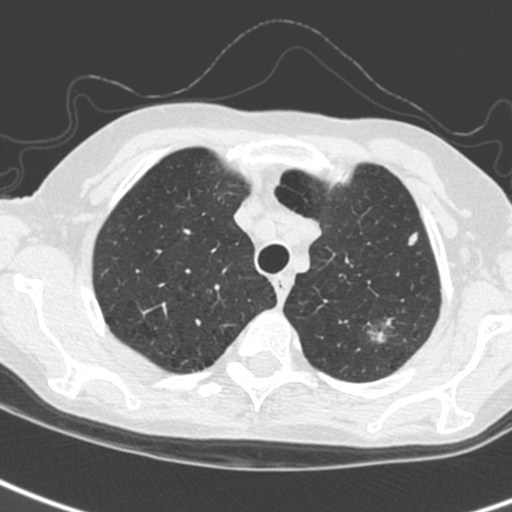
Low-dose screening chest CT, one axial slice. Position 210 of 242 along the scan axis. Lung window (W 1500 / L -600 HU). 512 × 512 image matrix, field of view 284 × 284 mm.
Annotated regions visible in this slice (expert manual segmentation):
- lesion 2 (tumor, upper lobe of left lung): bounding box (x1, y1, x2, y2) in pixels: (408, 232, 418, 246)